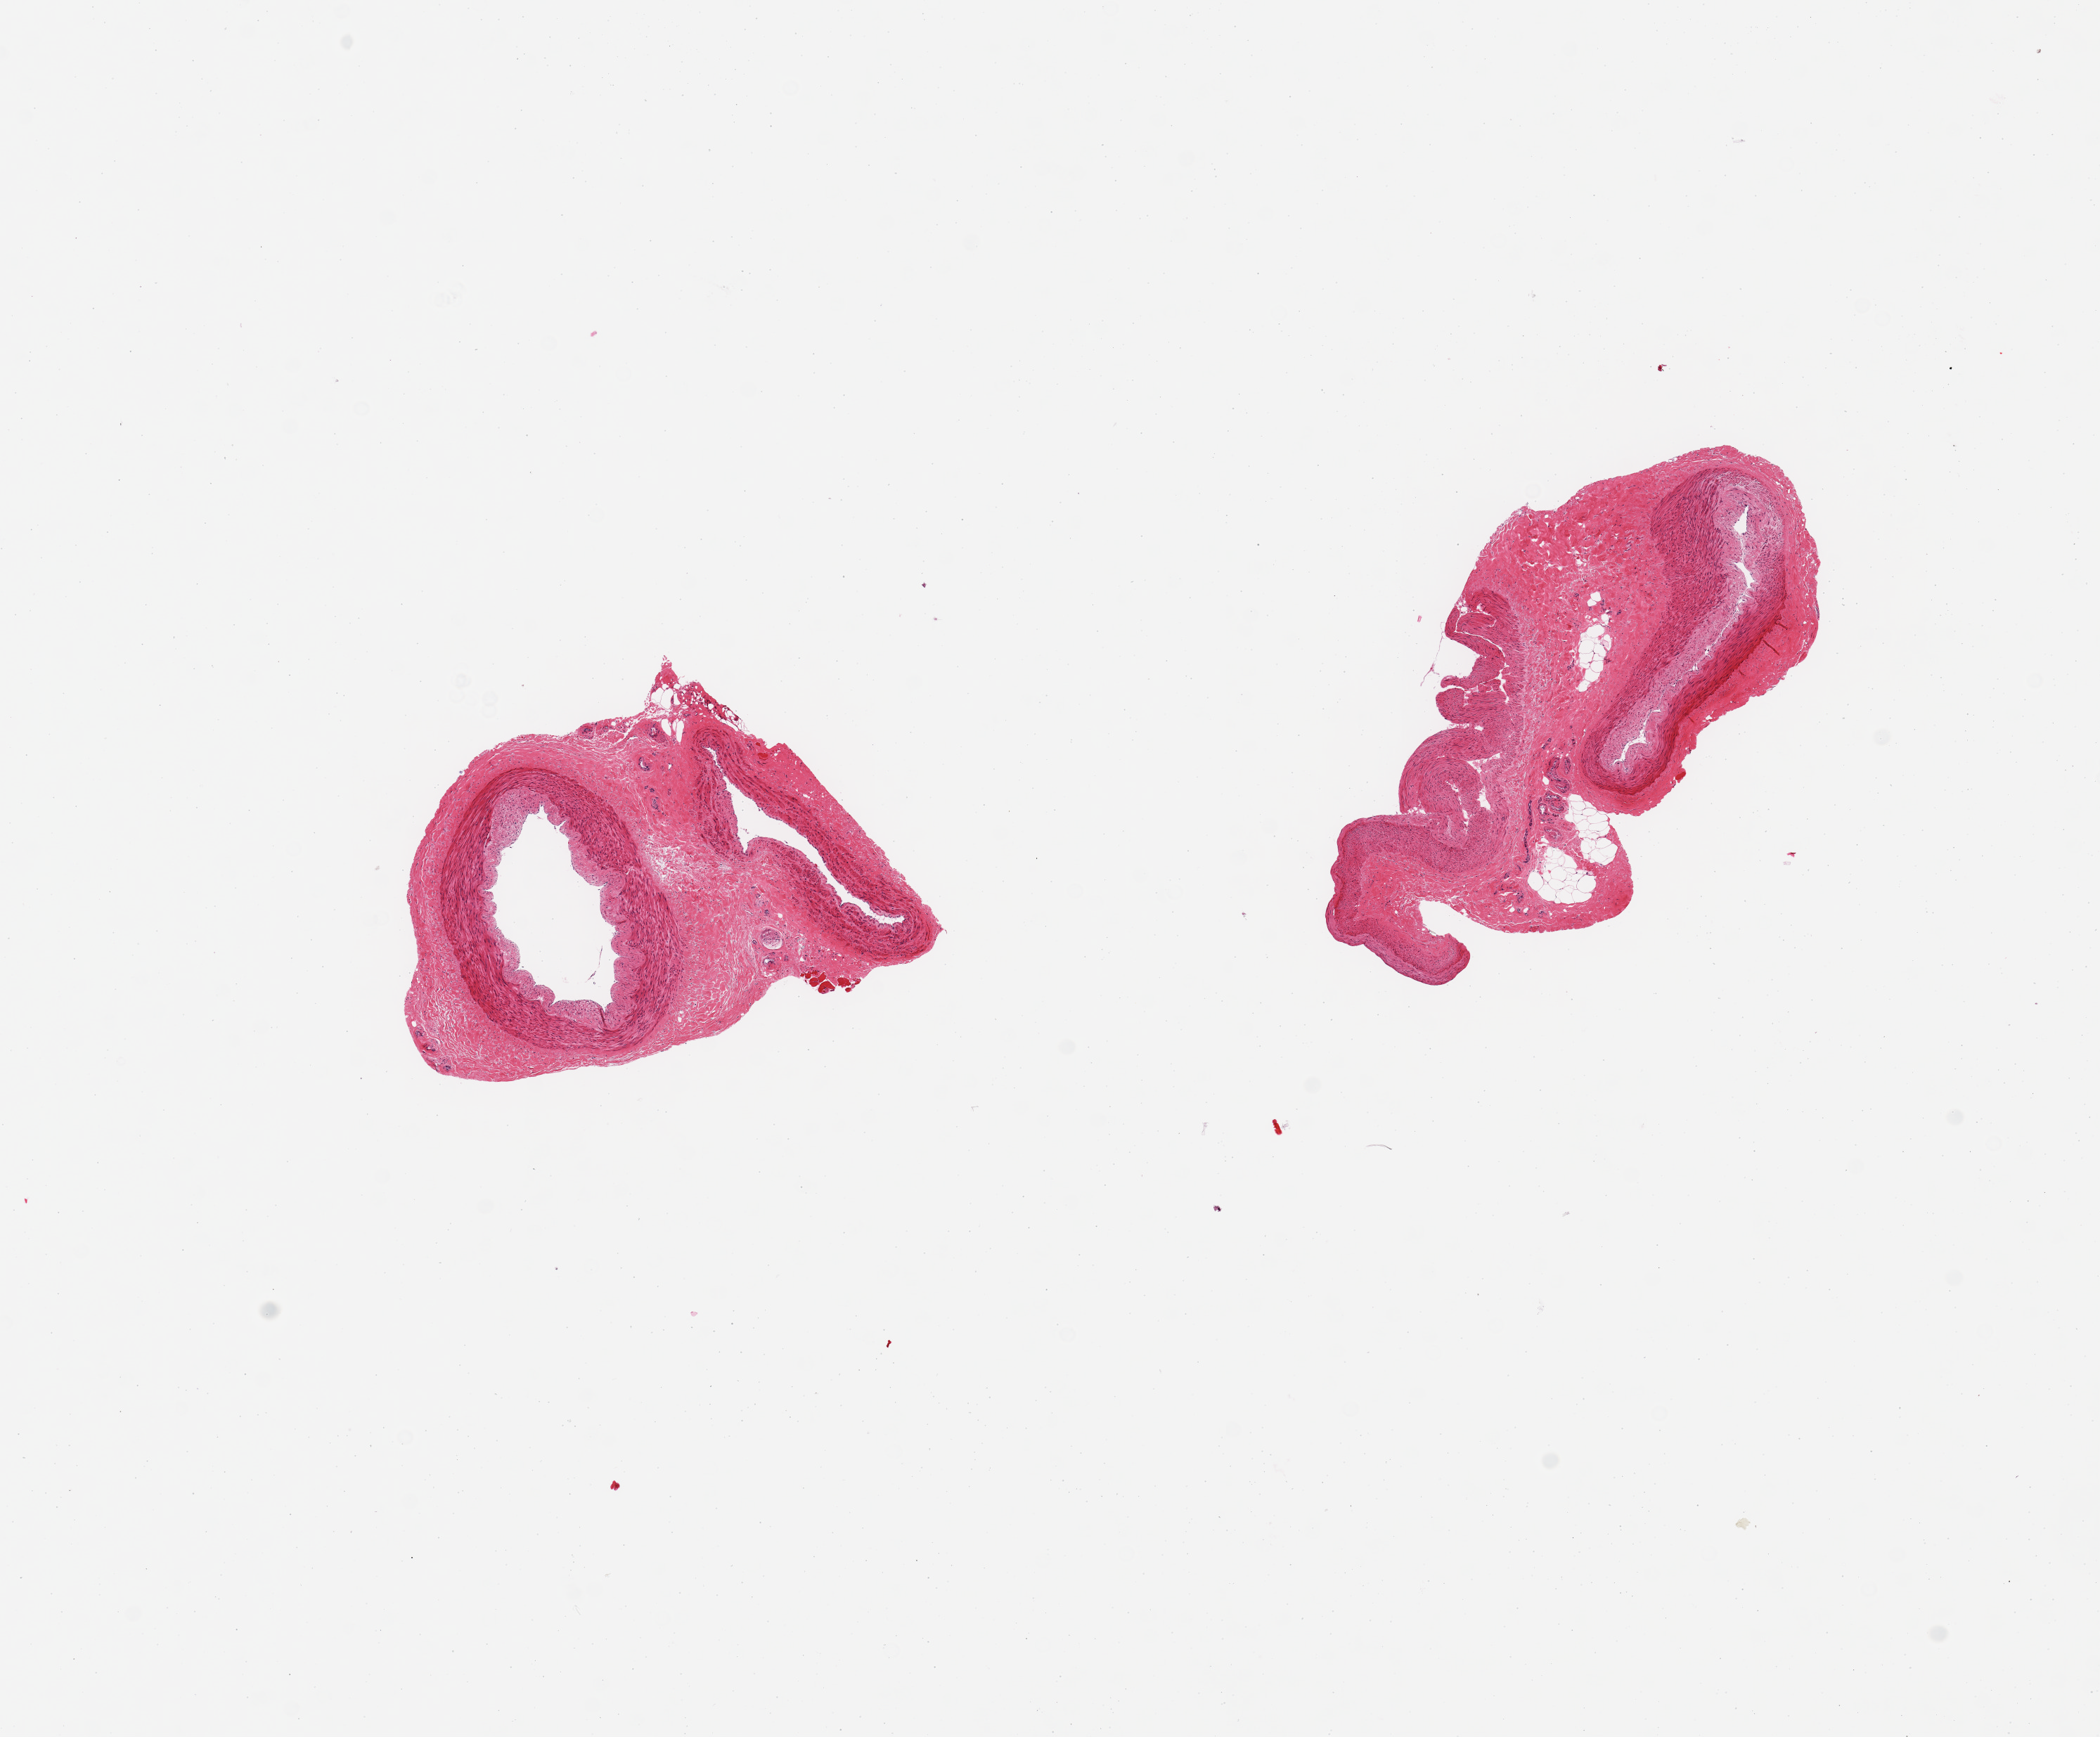
Whole-slide image, hematoxylin and eosin (H&E) stain — whole scanned area (about 11.8 x 9.8 mm) shown as a low-resolution overview, PAXgene-fixed paraffin-embedded (PFPE) section, target tissue: tibial artery, donor tissue sample. Donor: female.
Pathologist's review note for this sample: 2 pieces; several arteries; no lesions.